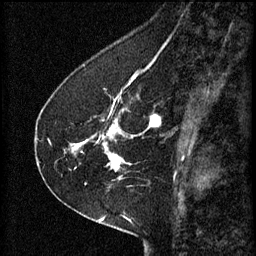
Breast MRI (dynamic contrast-enhanced), one sagittal slice. Slice 22 of 60 in the series (ordered by position). 3 images stored at this slice position (order not interpretable as contrast timing). 1.5 T. TE 4.2 ms, TR 8.2 ms. 256 × 256 image matrix, field of view 180 × 180 mm. Patient: female, 41 years.
Outlined on this slice (semi-automatically segmented with operator editing):
- analysis volume of interest (the breast-tissue region the enhancement analysis was run in; not a lesion): bounding box (x1, y1, x2, y2) in pixels: (71, 92, 157, 173)
- tumour enhancement mask (voxels above the 70 % enhancement threshold inside the analysis volume of interest): (72, 96, 157, 171)